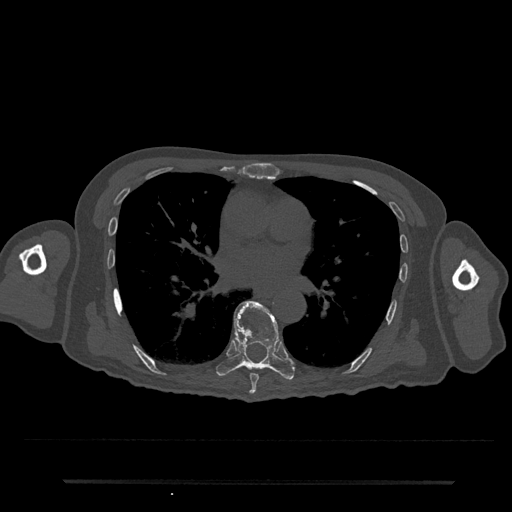
CT including the spine, one axial slice; slice 441 of 797 in the series (ordered by position); reconstruction kernel Br40s/3; 120 kVp; bone window (W 1800 / L 400 HU); 512 × 512 image matrix. Male patient, age 74 years. From the clinical record (not read from this slice): primary cancer: prostate.
Outlined on this slice (semi-automatically segmented with operator editing):
- T7 vertebra: bounding box [x1, y1, x2, y2] px = [249, 373, 259, 394]
- T8 vertebra: [216, 301, 295, 380]